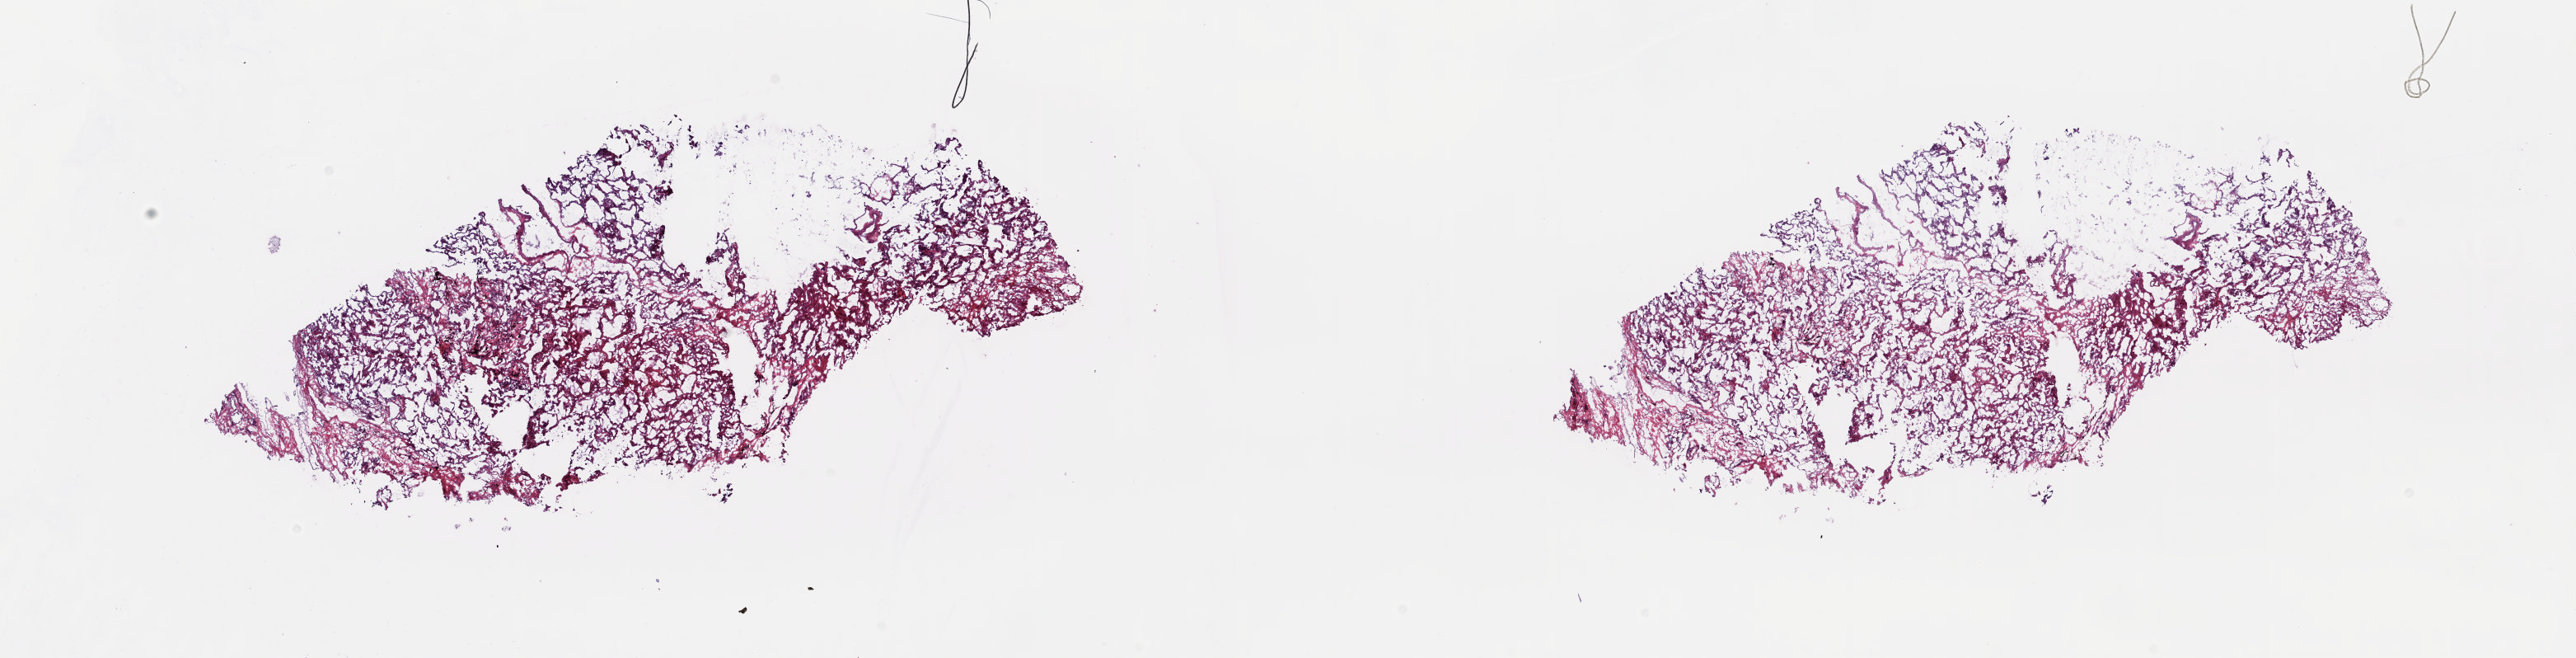
Digitized Hematoxylin and eosin (H&E) stained tissue section (whole slide) — shown as a low-resolution overview of the whole scanned area (about 24.8 x 6.3 mm, from a 20x scan), frozen section from the top of the tissue portion, lung, solid tissue normal (non-tumour tissue) sample. Male, age 51 years at initial diagnosis. Composition of this section per pathologist review: tumour cells 0%, tumour nuclei 0%, normal cells 70%, stromal cells 30%, necrosis 0%. Inflammatory infiltration, as recorded: lymphocyte infiltration 3%, monocyte infiltration 7%, neutrophil infiltration 1%.
- this section: solid tissue normal sample (biorepository sample class)
- patient diagnosis: Adenocarcinoma, NOS